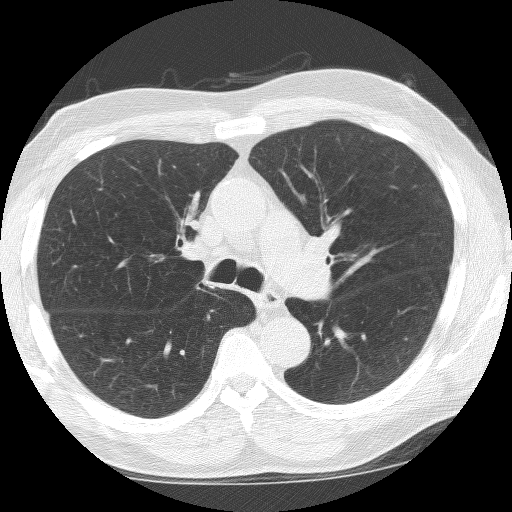
Low-dose screening chest CT, one axial slice; 120 kVp; lung window (W 1500 / L -600 HU); 2.5 mm slice thickness; 512 × 512 image matrix, field of view 323 × 323 mm.
Outlined on this slice (manually delineated by an expert):
- lesion 1 (tumor, lower lobe of left lung): bounding box (x1, y1, x2, y2) in pixels: (338, 339, 342, 344)